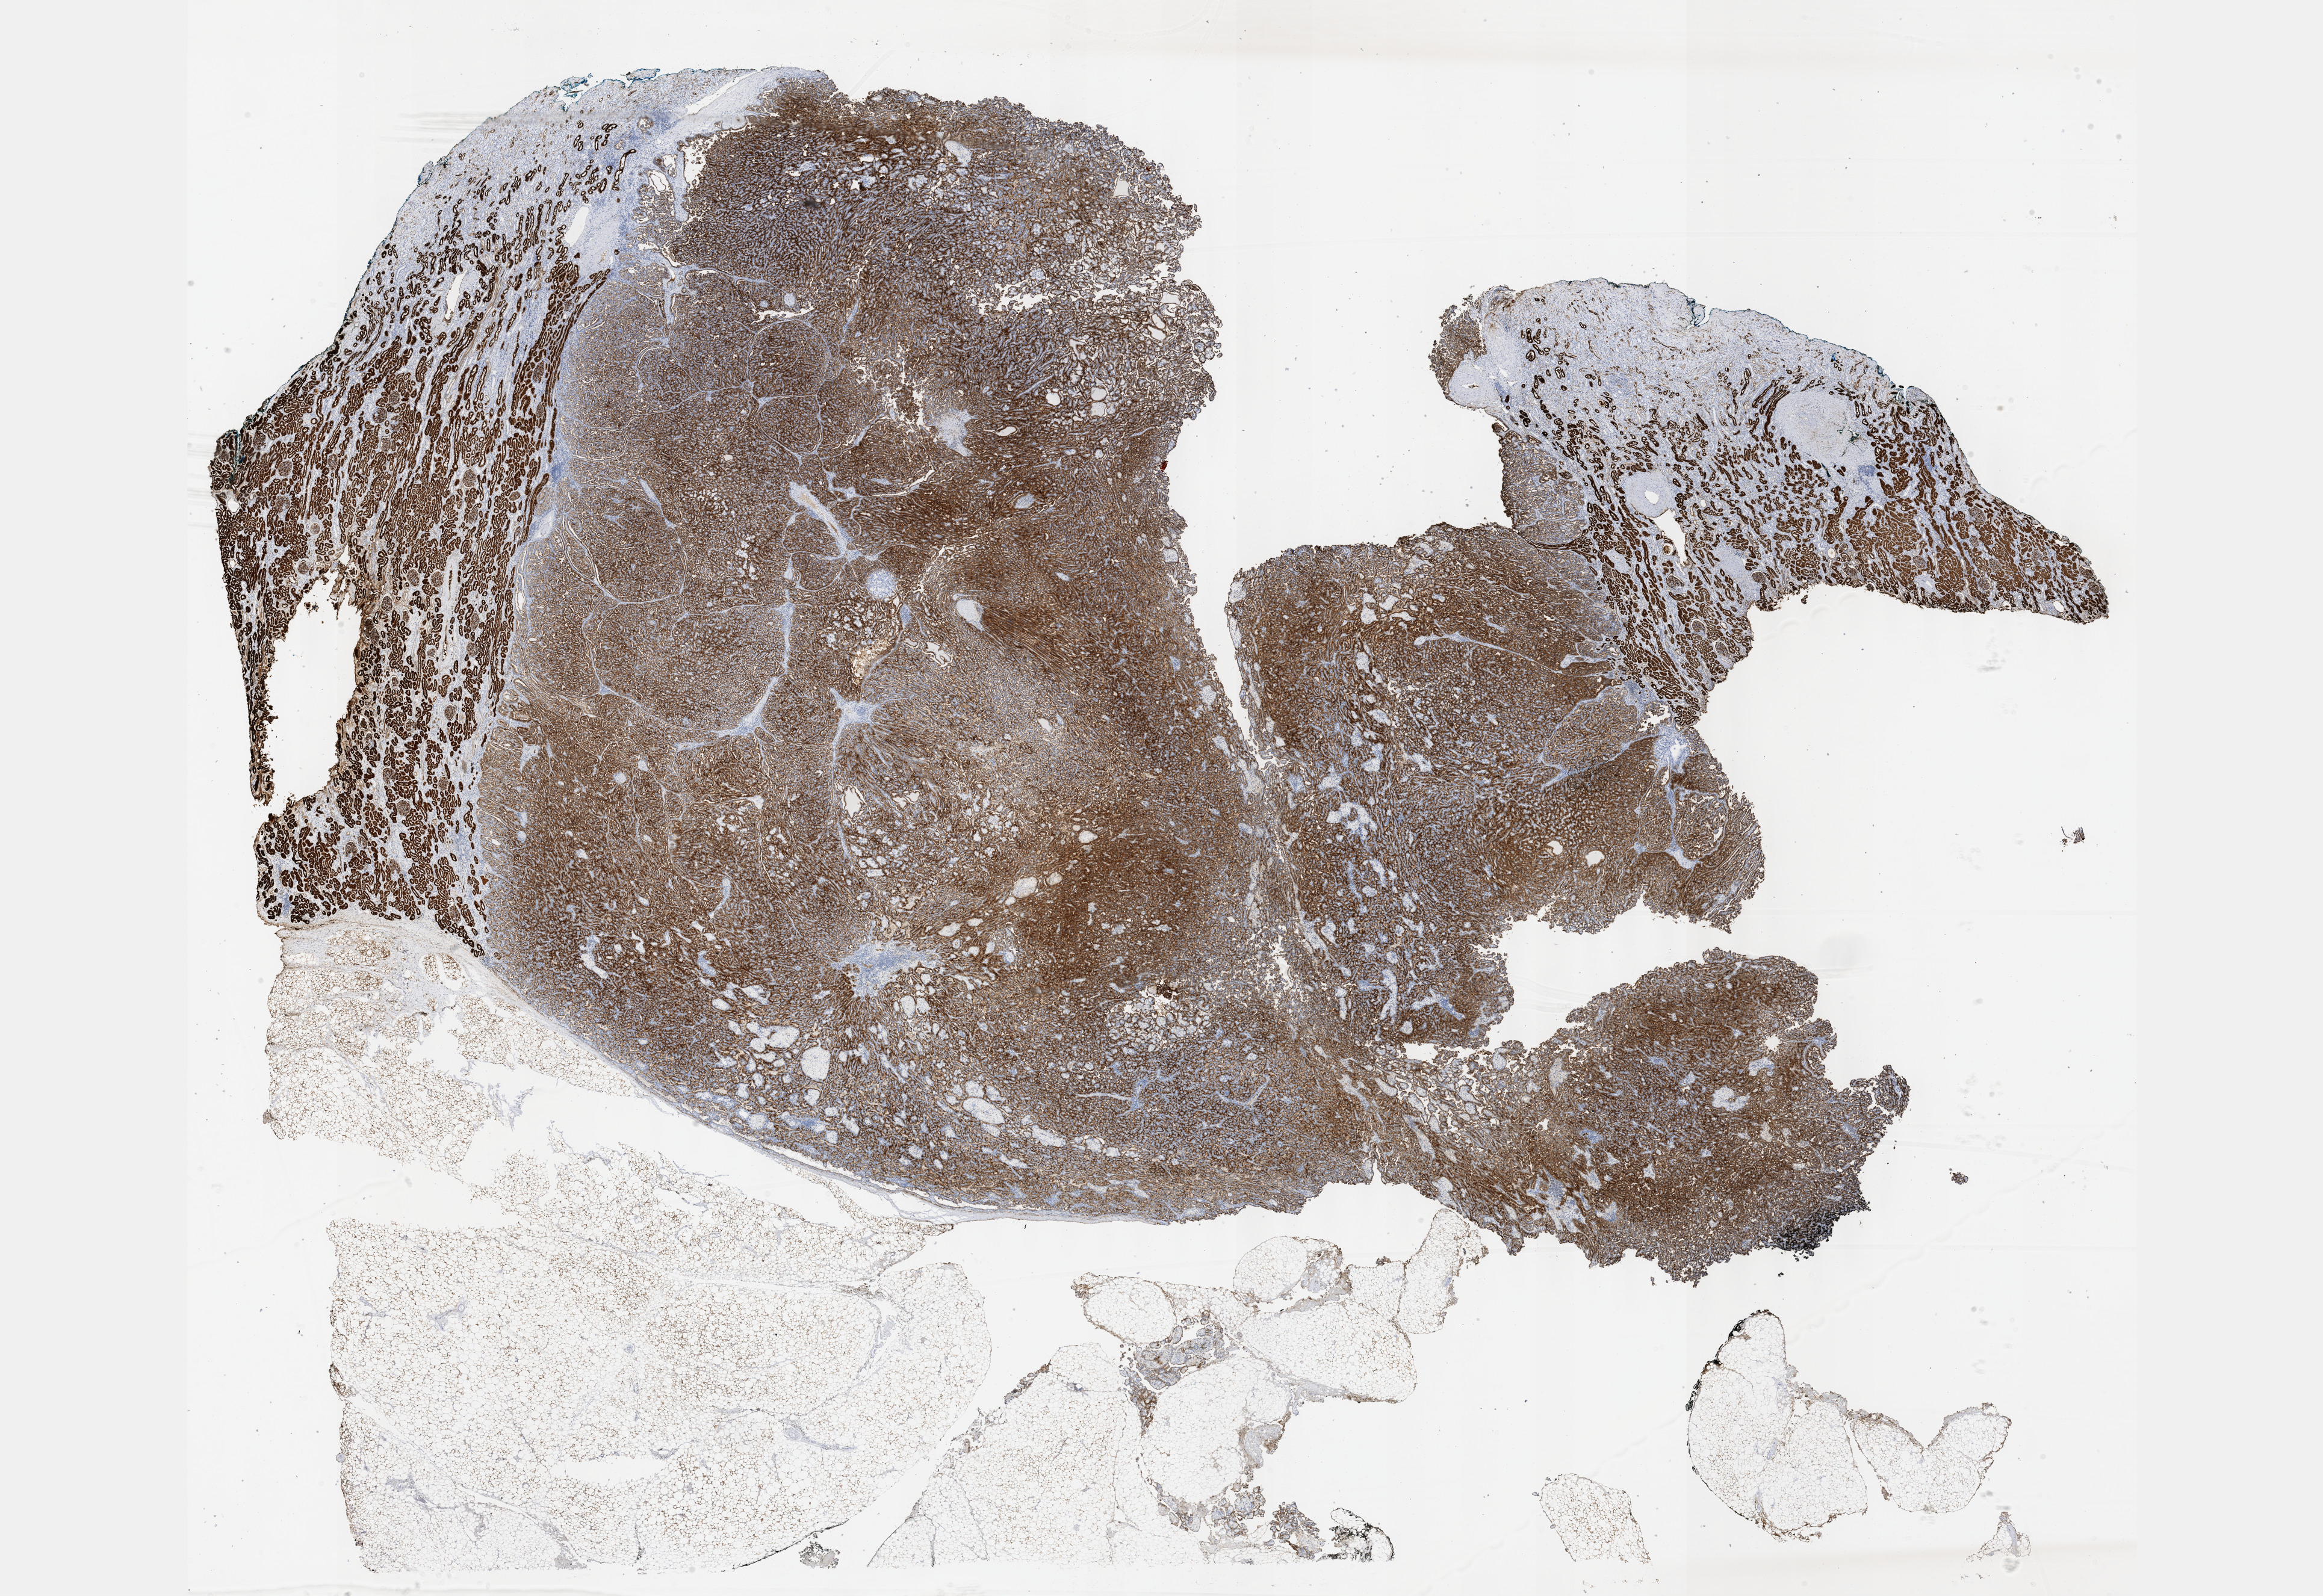
H&E whole-slide image — whole scanned area (about 31.2 x 21.4 mm, from a 40x scan) shown as a low-resolution overview; formalin-fixed paraffin-embedded (FFPE) diagnostic section; primary tumour sample from the kidney. Patient: male, age at initial diagnosis 65 years.
TNM: T1a NX MX. Diagnosis: Papillary adenocarcinoma, NOS. AJCC pathologic stage: I (7th edition). Laterality: right.